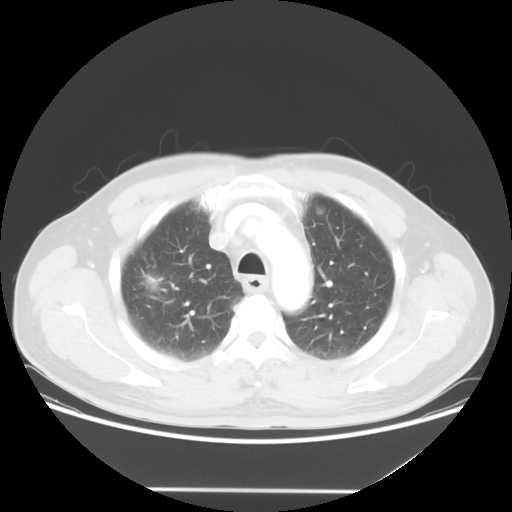
Chest CT, one axial slice; slice 41 of 54 in the series (ordered by position); lung window (W 1500 / L -600 HU); 5 mm slice thickness; 512 × 512 image matrix, field of view 416 × 416 mm. Patient: male, 65 years. From the clinical record (not read from this slice): clinical TNM (as recorded): T1c N1 M0.
Annotated regions visible in this slice (bounding box drawn by a radiologist):
- lung tumour (recorded histology: adenocarcinoma): bounding box [x1, y1, x2, y2] px = [139, 265, 163, 295]